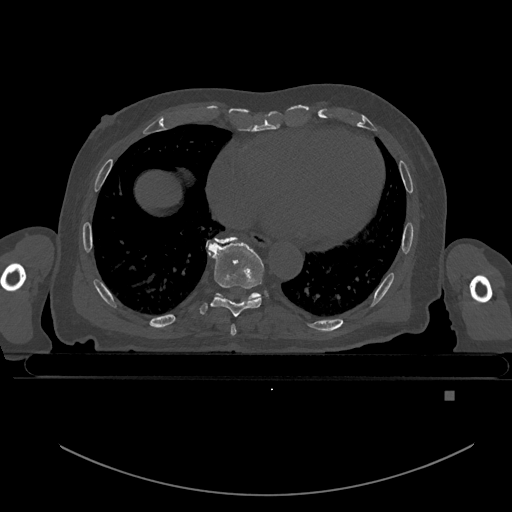
CT including the spine, one axial slice. Position 193 of 969 along the scan axis. Bone window (W 1800 / L 400 HU). 0.5 mm slice thickness. 512 × 512 image matrix. Male patient, age 82 years. Case-level facts recorded for this patient, not image findings: primary cancer: prostate; vertebrae with lytic lesions (as recorded): T11, T9, T8, T2.
Outlined on this slice (semi-automatic segmentation, software-assisted and operator-edited):
- T7 vertebra: bounding box [x1, y1, x2, y2] px = [231, 324, 236, 336]
- T8 vertebra: [199, 238, 263, 317]
- T9 vertebra: [208, 237, 261, 300]